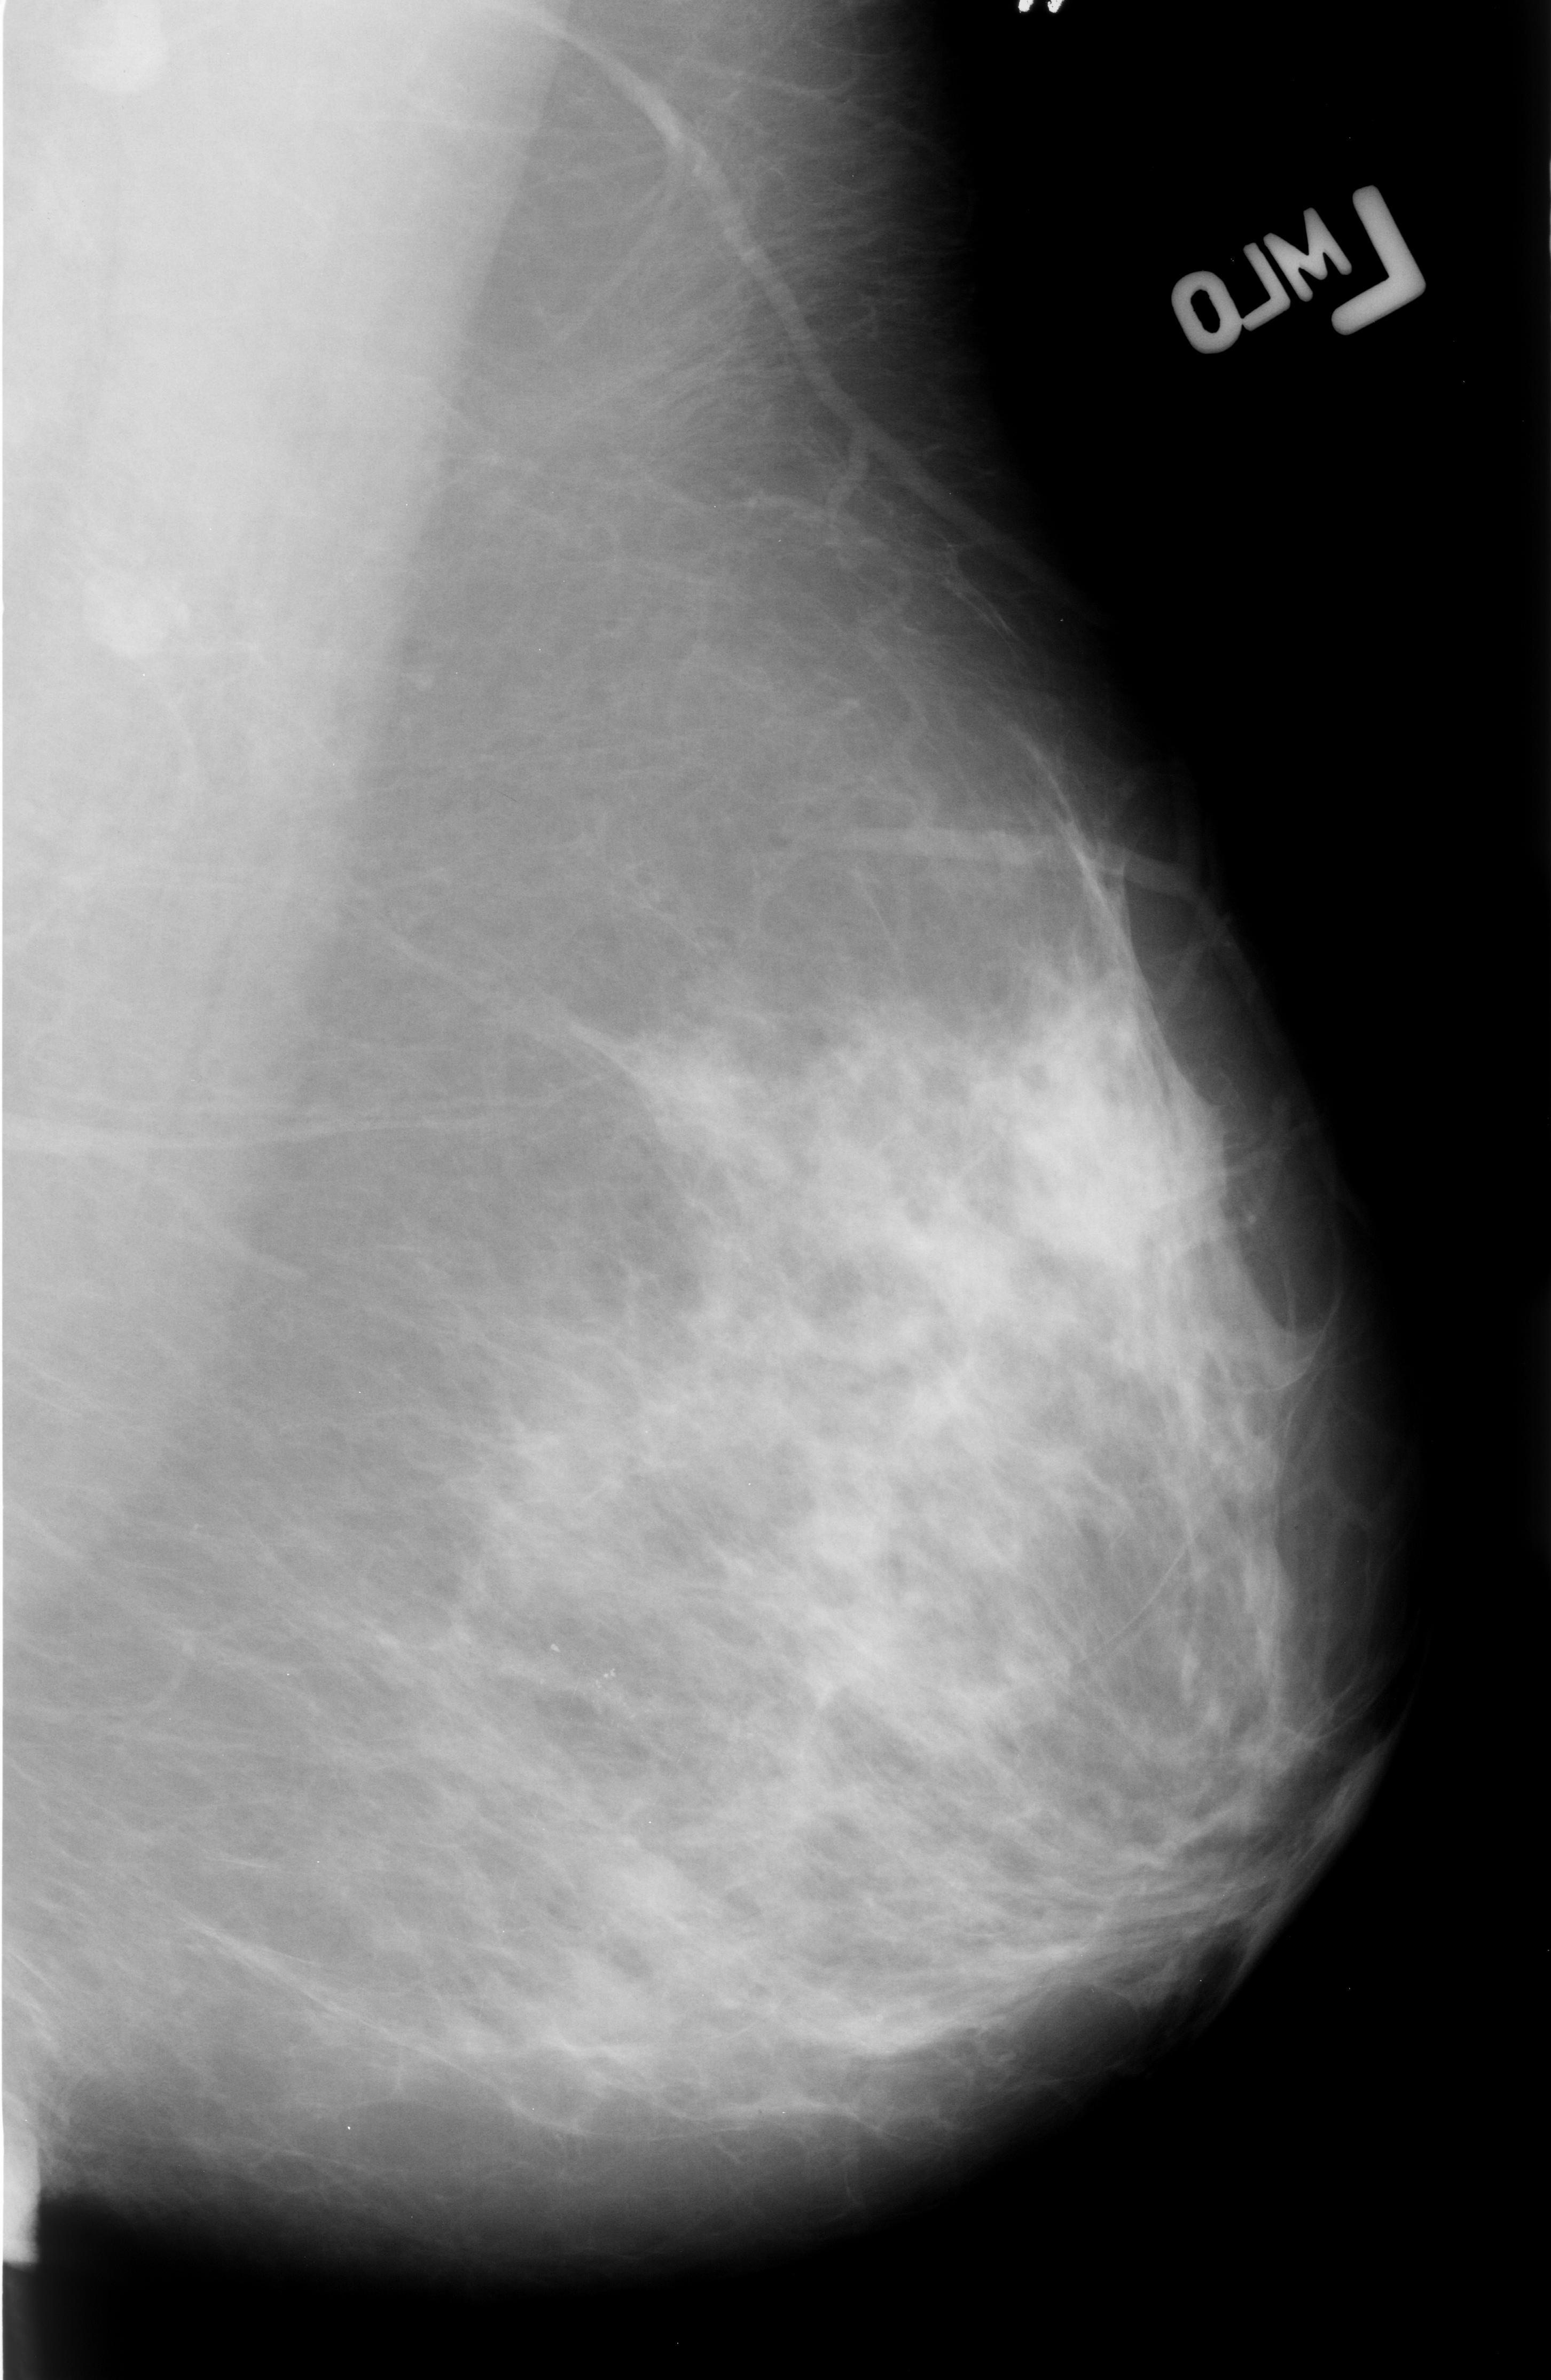
Scanned film-screen mammogram; left breast; mediolateral oblique (MLO) view; breast composition: scattered fibroglandular densities (BI-RADS density category 2 of 4); 1551 × 2380 image matrix.
Expert-marked regions of interest on this film, with their recorded descriptors:
- calcifications, morphology pleomorphic, distribution clustered; BI-RADS assessment category 4; pathology result (as recorded, not read from the image): malignant: bounding box [x1, y1, x2, y2] px = [534, 1627, 646, 1744]